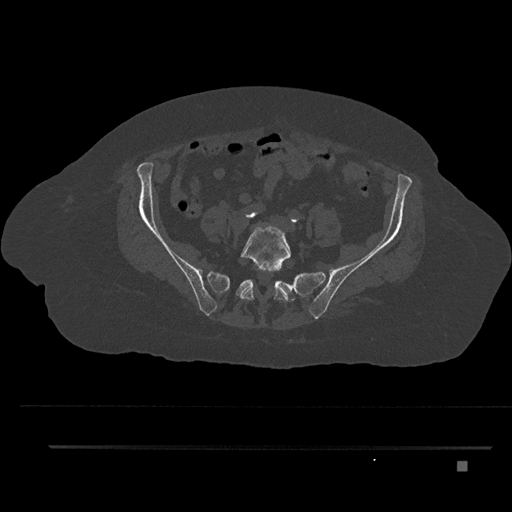
CT including the spine, one axial slice; position 26 of 797 along the scan axis; reconstruction kernel Br40s/3; bone window (W 1800 / L 400 HU); 0.5 mm slice thickness; 512 × 512 image matrix, field of view 437 × 437 mm. Female patient, age 76 years. Case-level facts recorded for this patient, not image findings: primary cancer: lung.
Annotated regions visible in this slice (semi-automatic segmentation, software-assisted and operator-edited):
- L5 vertebra: box from (x=240, y=224) to (x=291, y=318) px